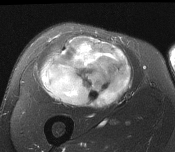
MRI of an extremity soft-tissue mass, one axial slice; position 91 of 116 along the scan axis; T2-weighted fat-saturated; MR volume resampled by the dataset authors to the PET/CT grid (not the native acquisition matrix); 3.27 mm slice thickness; 175 × 152 image matrix. Male patient. From the clinical record (not read from this slice): histological type: pleiomorphic leiomyosarcoma; grade: intermediate; site of the primary tumour: right thigh.
Annotated regions visible in this slice (expert contour drawn on MRI and transferred to this co-registered scan by the dataset authors):
- gross tumour volume including surrounding oedema: bounding box [x1, y1, x2, y2] px = [40, 38, 132, 107]
- gross tumour volume (mass): [40, 38, 132, 107]